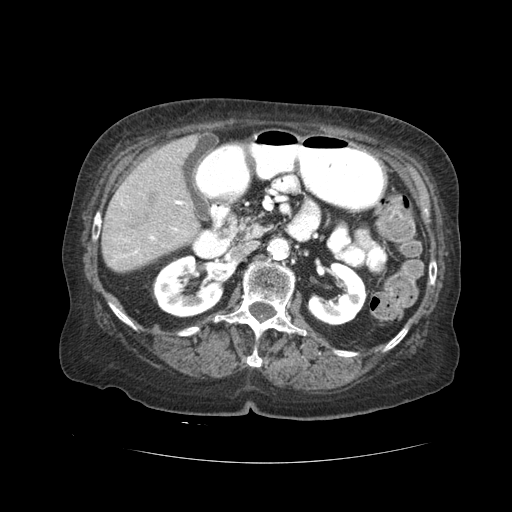
Contrast-enhanced abdominal CT (liver protocol), one axial slice; position 9 of 59 along the scan axis; soft-tissue window (W 400 / L 40 HU); 512 × 512 image matrix. Case-level facts recorded for this patient, not image findings: diagnosis: hepatocellular carcinoma (patient treated with transarterial chemoembolisation; whether this scan precedes or follows treatment is not stated here); TNM stage (as recorded): Stage-I; Child-Pugh class: A.
Outlined on this slice (semi-automatically segmented with operator editing):
- liver parenchyma outside the tumour (the mass and vessels are separate outlines, so this box may not span the whole liver): bounding box [x1, y1, x2, y2] px = [102, 134, 198, 272]
- liver vessels: [122, 200, 184, 257]